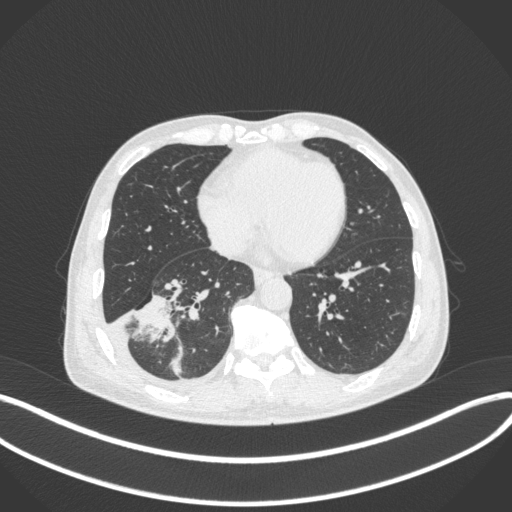
Chest CT, one axial slice. Slice 137 of 385 in the series (ordered by position). Lung window (W 1500 / L -600 HU). 512 × 512 image matrix. Patient: male, 64 years. From the clinical record (not read from this slice): clinical TNM (as recorded): T3 N0 M0; histopathological grade: G2-3.
Structures marked on this image (rectangle marked by the reading radiologist):
- lung tumour (recorded histology: adenocarcinoma): bounding box (x1, y1, x2, y2) in pixels: (131, 291, 177, 345)